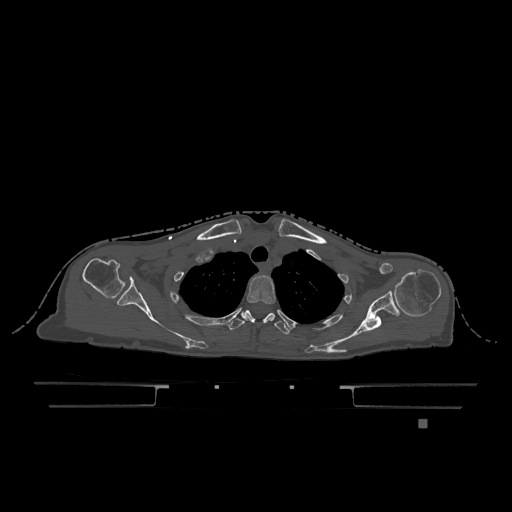
CT including the spine, one axial slice; position 946 of 1317 along the scan axis; bone window (W 1800 / L 400 HU); 0.5 mm slice thickness; 512 × 512 image matrix, field of view 500 × 500 mm. Female patient, age 74 years. From the clinical record (not read from this slice): primary cancer: lung.
Annotated regions visible in this slice (semi-automatic segmentation, software-assisted and operator-edited):
- T2 vertebra: bounding box <247,275,276,304> (left, top, right, bottom; pixels)
- T3 vertebra: <229,310,290,335>
- T6 vertebra: <267,313,275,318>